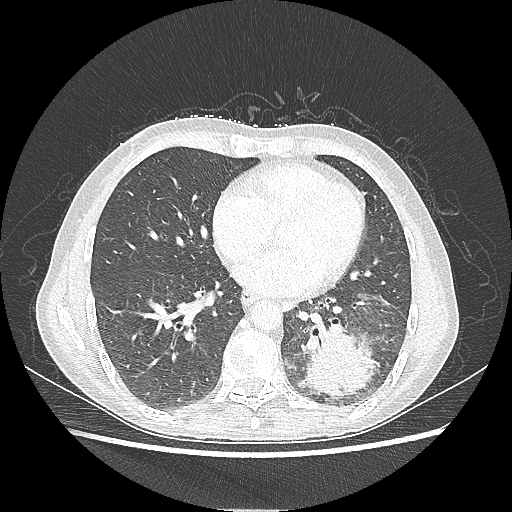
Chest CT, one axial slice; slice 90 of 220 in the series (ordered by position); reconstruction kernel LUNG; 80 kVp; lung window (W 1500 / L -600 HU); 512 × 512 image matrix, field of view 360 × 360 mm. Female patient, age 53 years. From the clinical record (not read from this slice): clinical TNM (as recorded): T3 N0 M0.
Structures marked on this image (bounding box drawn by a radiologist):
- lung tumour (recorded histology: adenocarcinoma): bounding box <298,322,381,399> (left, top, right, bottom; pixels)